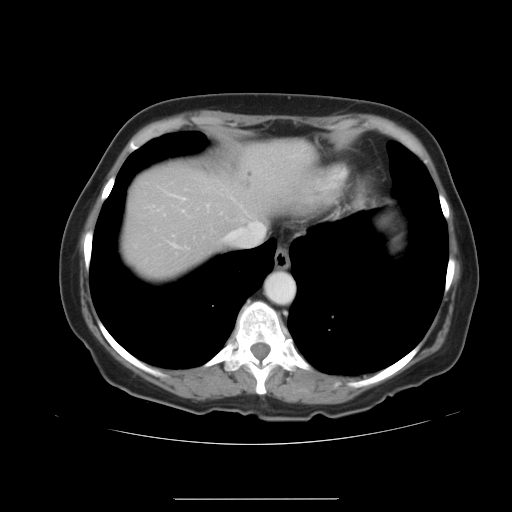
Contrast-enhanced abdominal CT, one axial slice. Slice 34 of 41 in the series (ordered by position). 120 kVp. Intravenous contrast given. Soft-tissue window (W 400 / L 40 HU). 5 mm slice thickness. 512 × 512 image matrix. Female patient, age 63 years. From the clinical record (not read from this slice): diagnosis: colorectal cancer liver metastases, imaged before liver resection; multiple liver metastases: yes.
Outlined on this slice (outlined manually by an expert reader):
- hepatic veins: bounding box <228,223,261,239> (left, top, right, bottom; pixels)
- liver: <122,142,305,283>
- planned liver remnant (the part of the liver to remain after resection): <122,142,305,283>
- liver metastasis: <242,180,252,189>